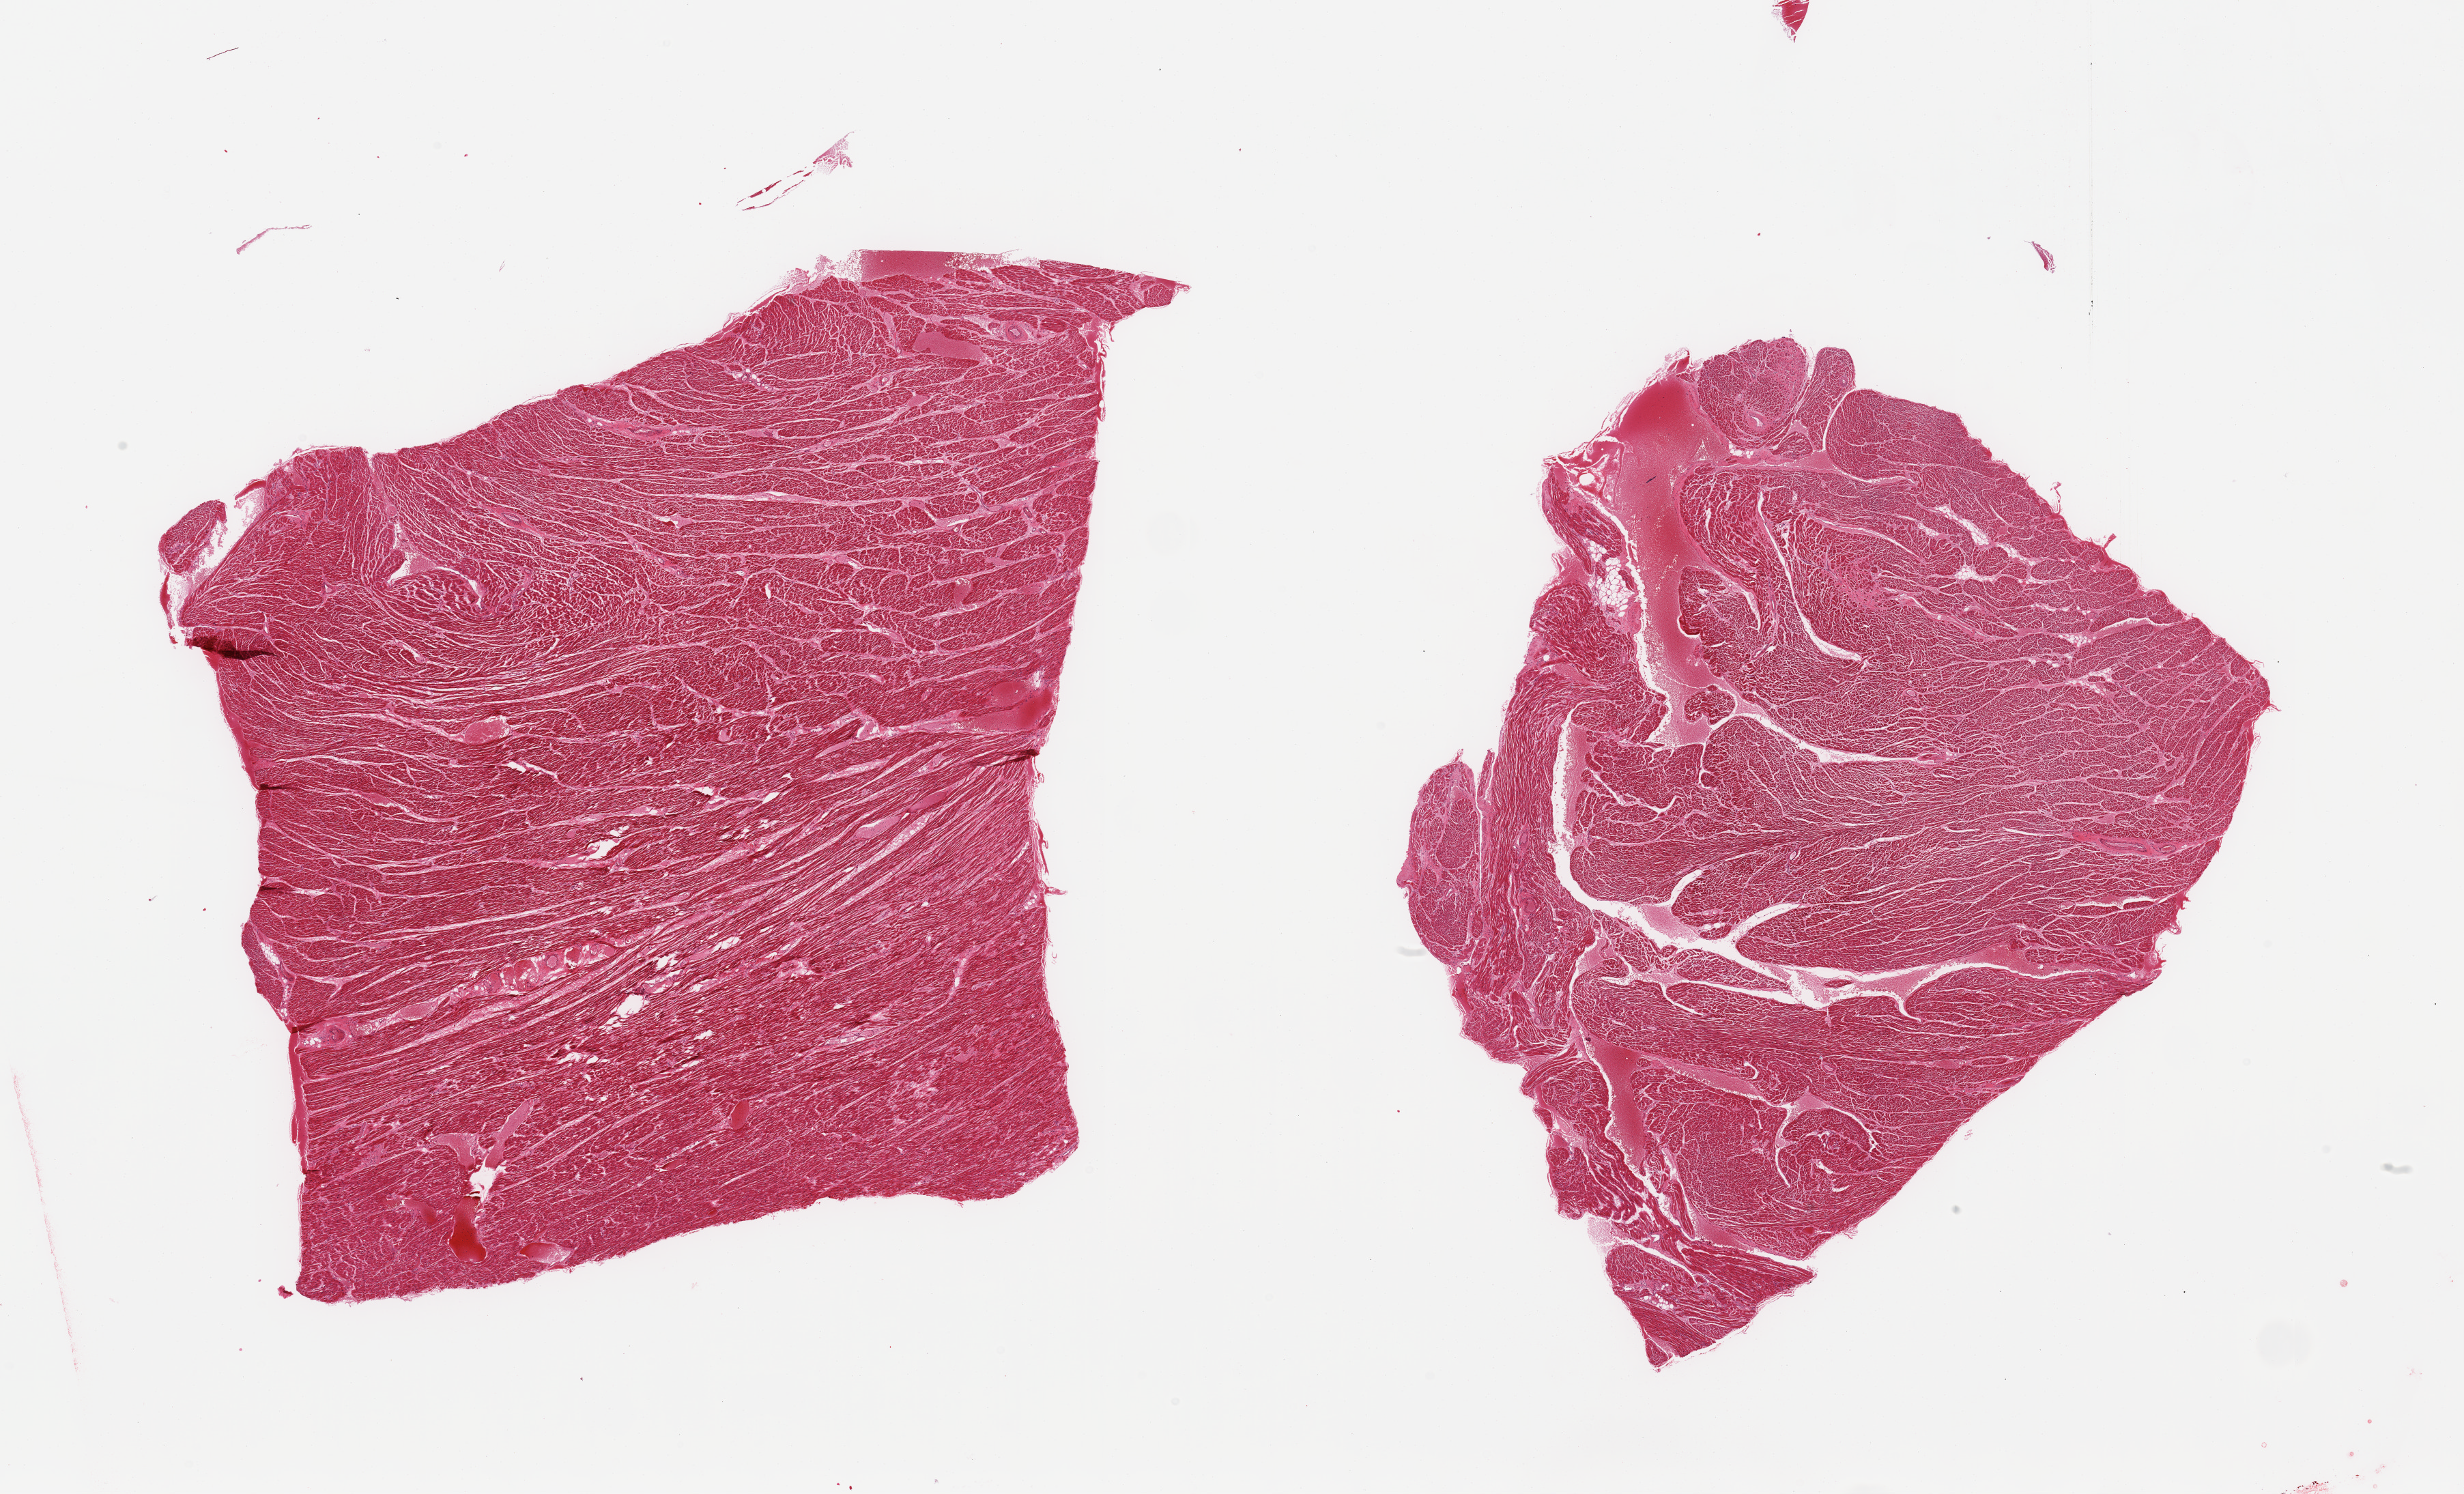
Digitized haematoxylin and eosin-stained section — whole scanned area (about 28.5 x 17.3 mm) shown as a low-resolution overview, PAXgene-fixed paraffin-embedded (PFPE) section, target tissue: heart, tissue donor sample. Donor: female.
Review note (as recorded): 2 pieces, moderate interstitial fibrosis/chronic ischemic damage; microinfarct, ~0.6mm.